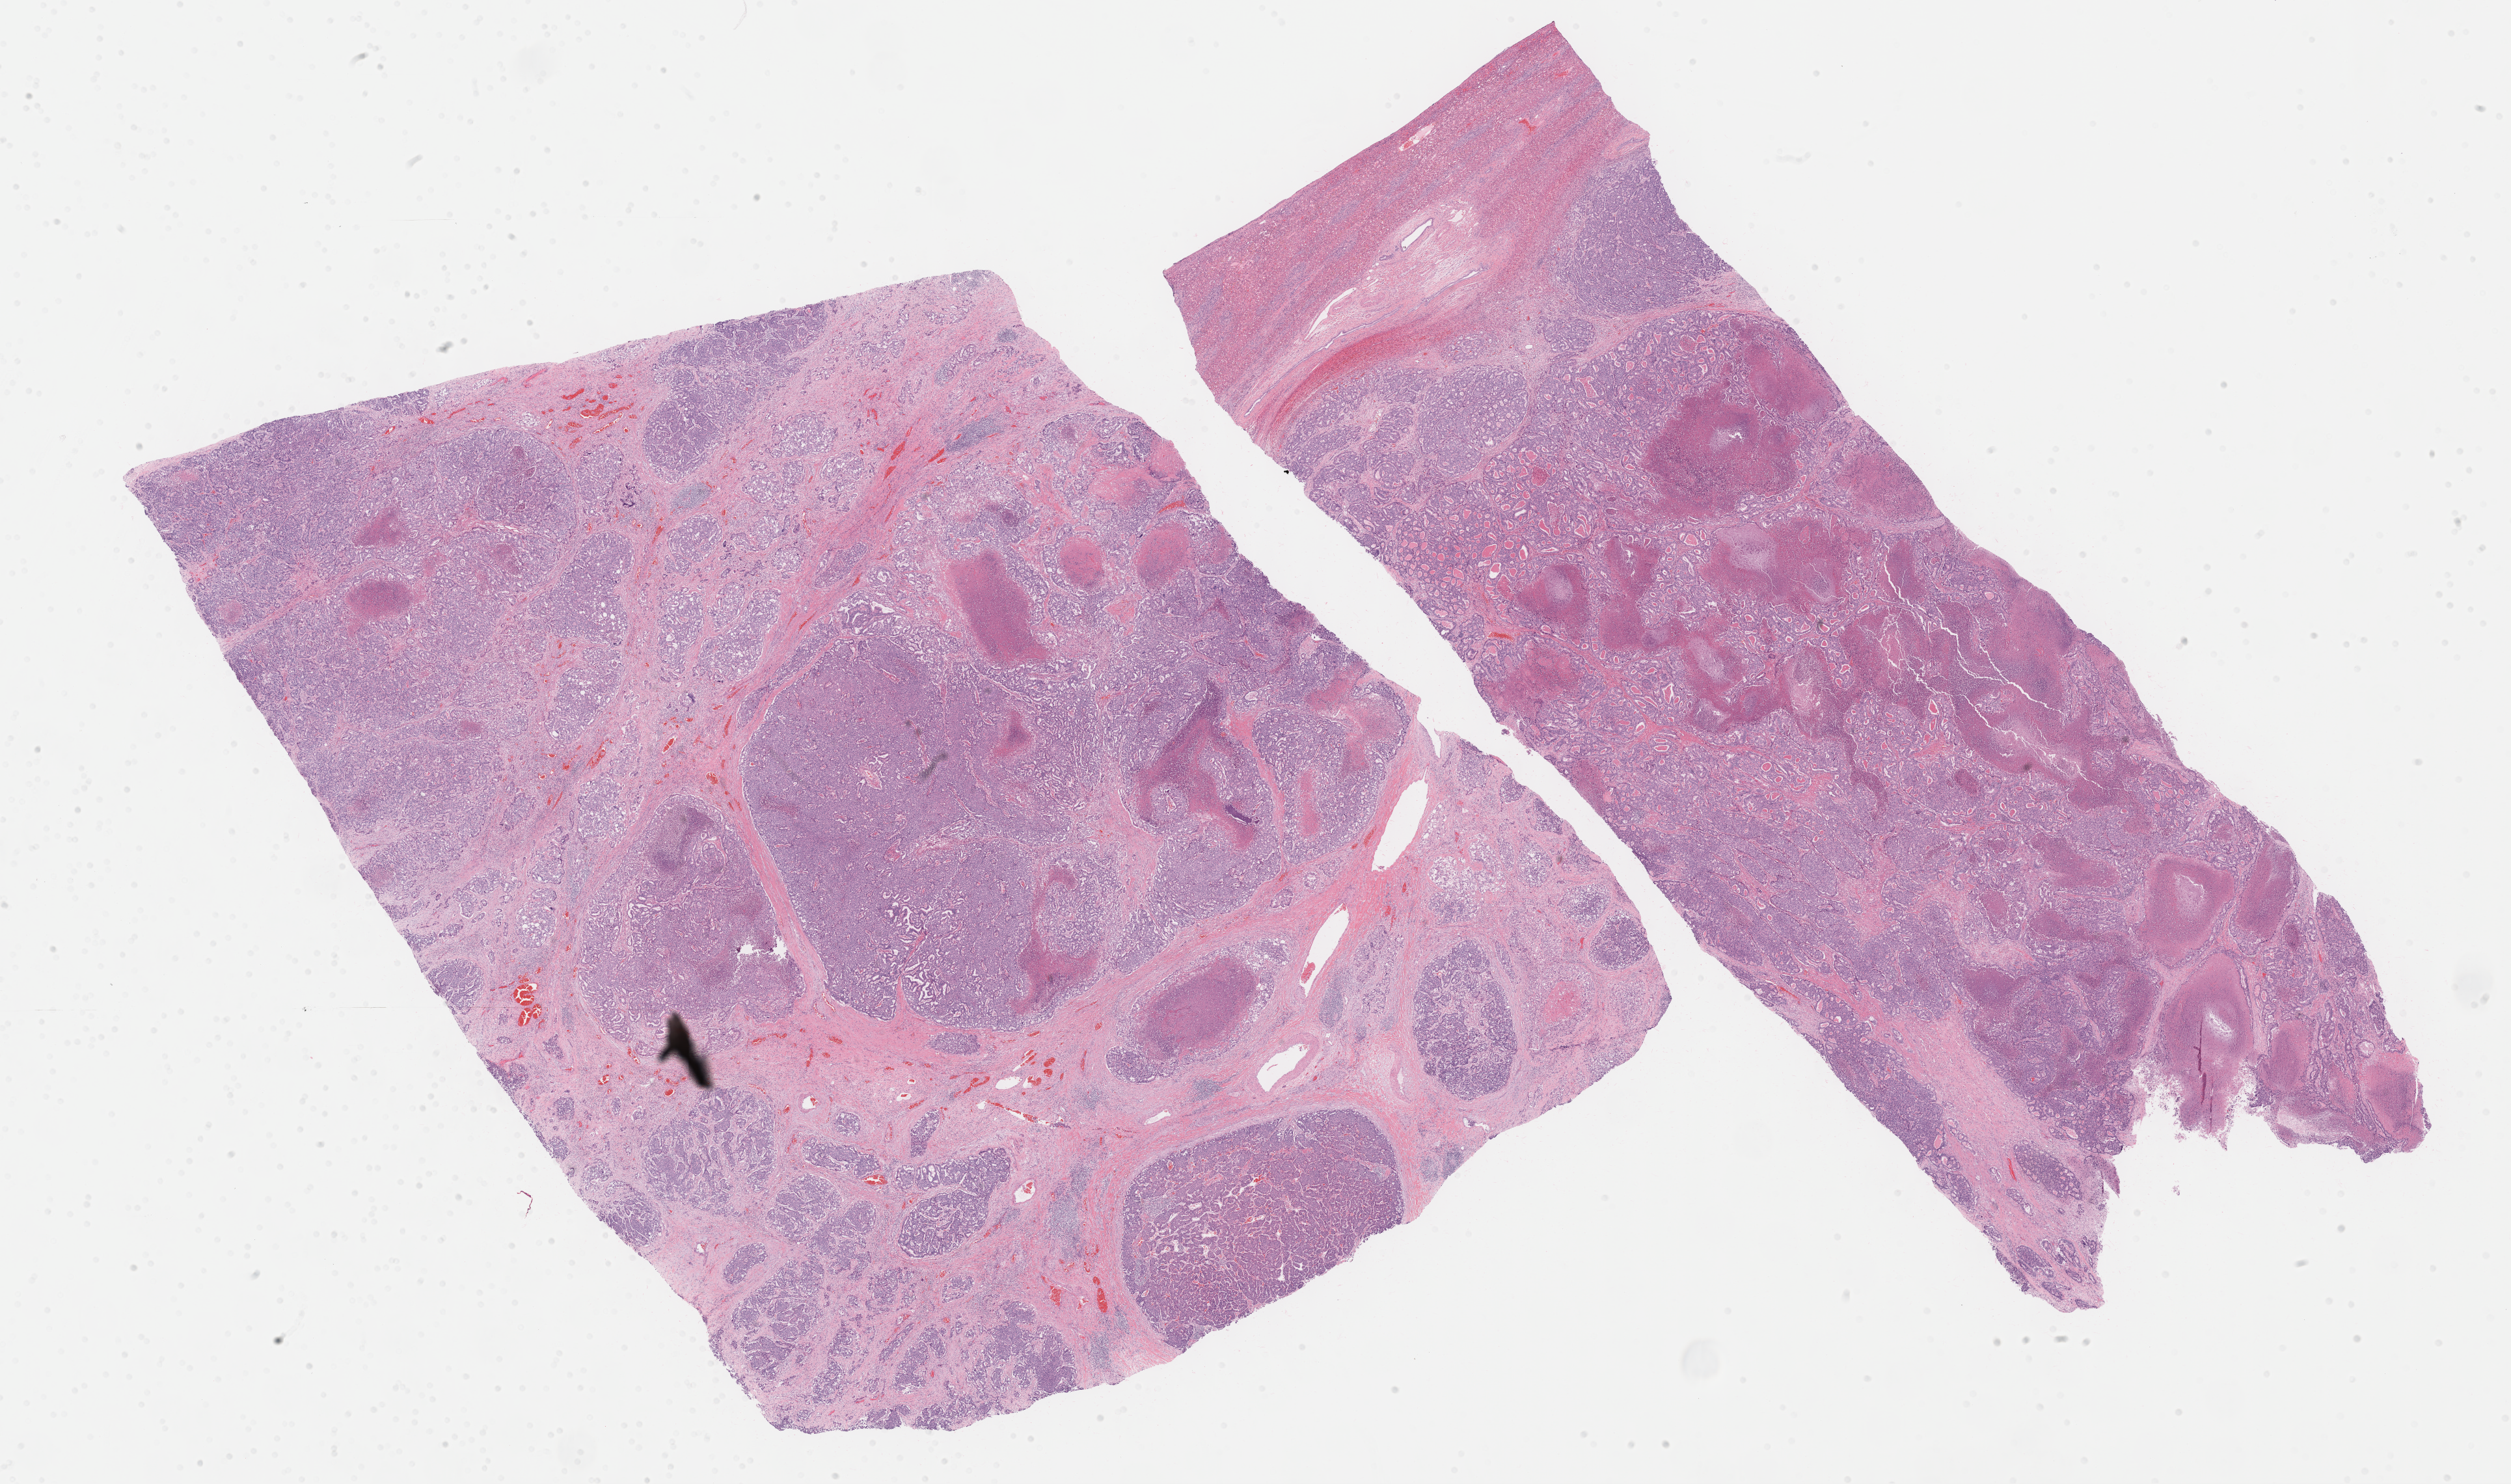
Whole-slide histology image, Hematoxylin and eosin (H&E) stained — shown as a low-resolution overview of the whole scanned area (about 31.2 x 18.4 mm, acquisition: 40x scan). Formalin-fixed paraffin-embedded (FFPE) diagnostic section. Sample: primary tumour, liver. Female patient; age at initial diagnosis 62 years. Histologic grade: G2 (moderately differentiated).
* histologic diagnosis: Combined hepatocellular carcinoma and cholangiocarcinoma
* TNM: T2b N0 M0
* AJCC pathologic stage: II (7th edition)